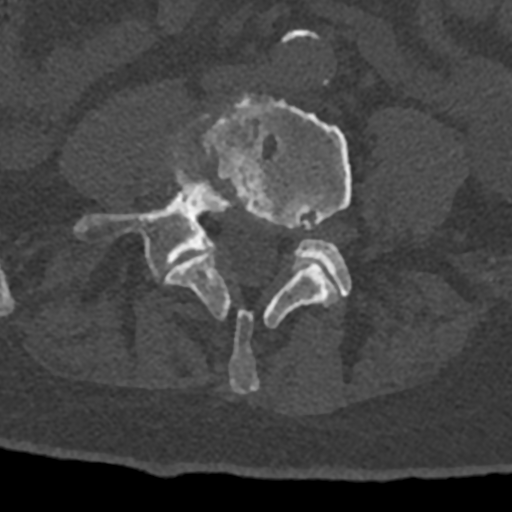
CT including the spine, one axial slice; position 234 of 797 along the scan axis; 120 kVp; bone window (W 1800 / L 400 HU); 0.5 mm slice thickness; 512 × 512 image matrix, field of view 160 × 160 mm. Male patient, age 74 years. From the clinical record (not read from this slice): primary cancer: renal; vertebrae with lytic lesions (as recorded): T10, L1, L2, L3, L4, L5.
Structures marked on this image (semi-automatic segmentation, software-assisted and operator-edited):
- L4 vertebra: bounding box <164,94,352,394> (left, top, right, bottom; pixels)
- L5 vertebra: <73,146,351,297>